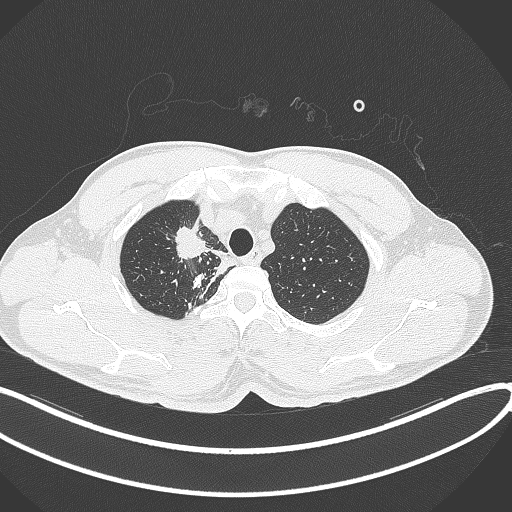
Chest CT, one axial slice. Slice 323 of 391 in the series (ordered by position). Reconstruction kernel B70f. 120 kVp. Lung window (W 1500 / L -600 HU). 1 mm slice thickness. 512 × 512 image matrix, field of view 400 × 400 mm. Male patient, age 48 years. From the clinical record (not read from this slice): clinical TNM (as recorded): T1c N1 M1.
Outlined on this slice (rectangle marked by the reading radiologist):
- lung tumour (recorded histology: adenocarcinoma): bounding box <167,226,209,264> (left, top, right, bottom; pixels)